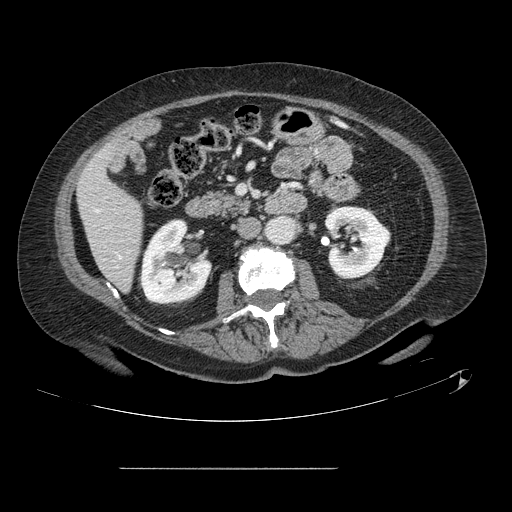
Contrast-enhanced abdominal CT, one axial slice; slice 38 of 148 in the series (ordered by position); 120 kVp; intravenous contrast given; soft-tissue window (W 400 / L 40 HU); 2.5 mm slice thickness; 512 × 512 image matrix. Female patient, age 75 years. From the clinical record (not read from this slice): diagnosis: colorectal cancer liver metastases, imaged before liver resection; multiple liver metastases: no; largest metastasis: 2.4 cm; chemotherapy before resection: no.
Outlined on this slice (expert manual segmentation):
- hepatic veins: bounding box (x1, y1, x2, y2) in pixels: (96, 209, 121, 258)
- liver: (79, 147, 143, 291)
- planned liver remnant (the part of the liver to remain after resection): (79, 144, 143, 291)